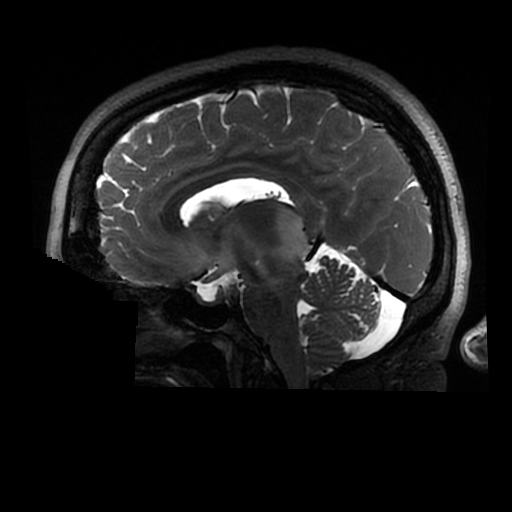
Brain MRI from a brain-tumour surgery series, one sagittal slice. Slice 161 of 320 in the series (ordered by position). 512 × 512 image matrix. From the clinical record (not read from this slice): histopathology: Astrocytoma; WHO grade: 2; IDH mutation: yes.
Outlined on this slice (outlined manually by an expert reader):
- tumour: bounding box [x1, y1, x2, y2] px = [273, 205, 308, 266]